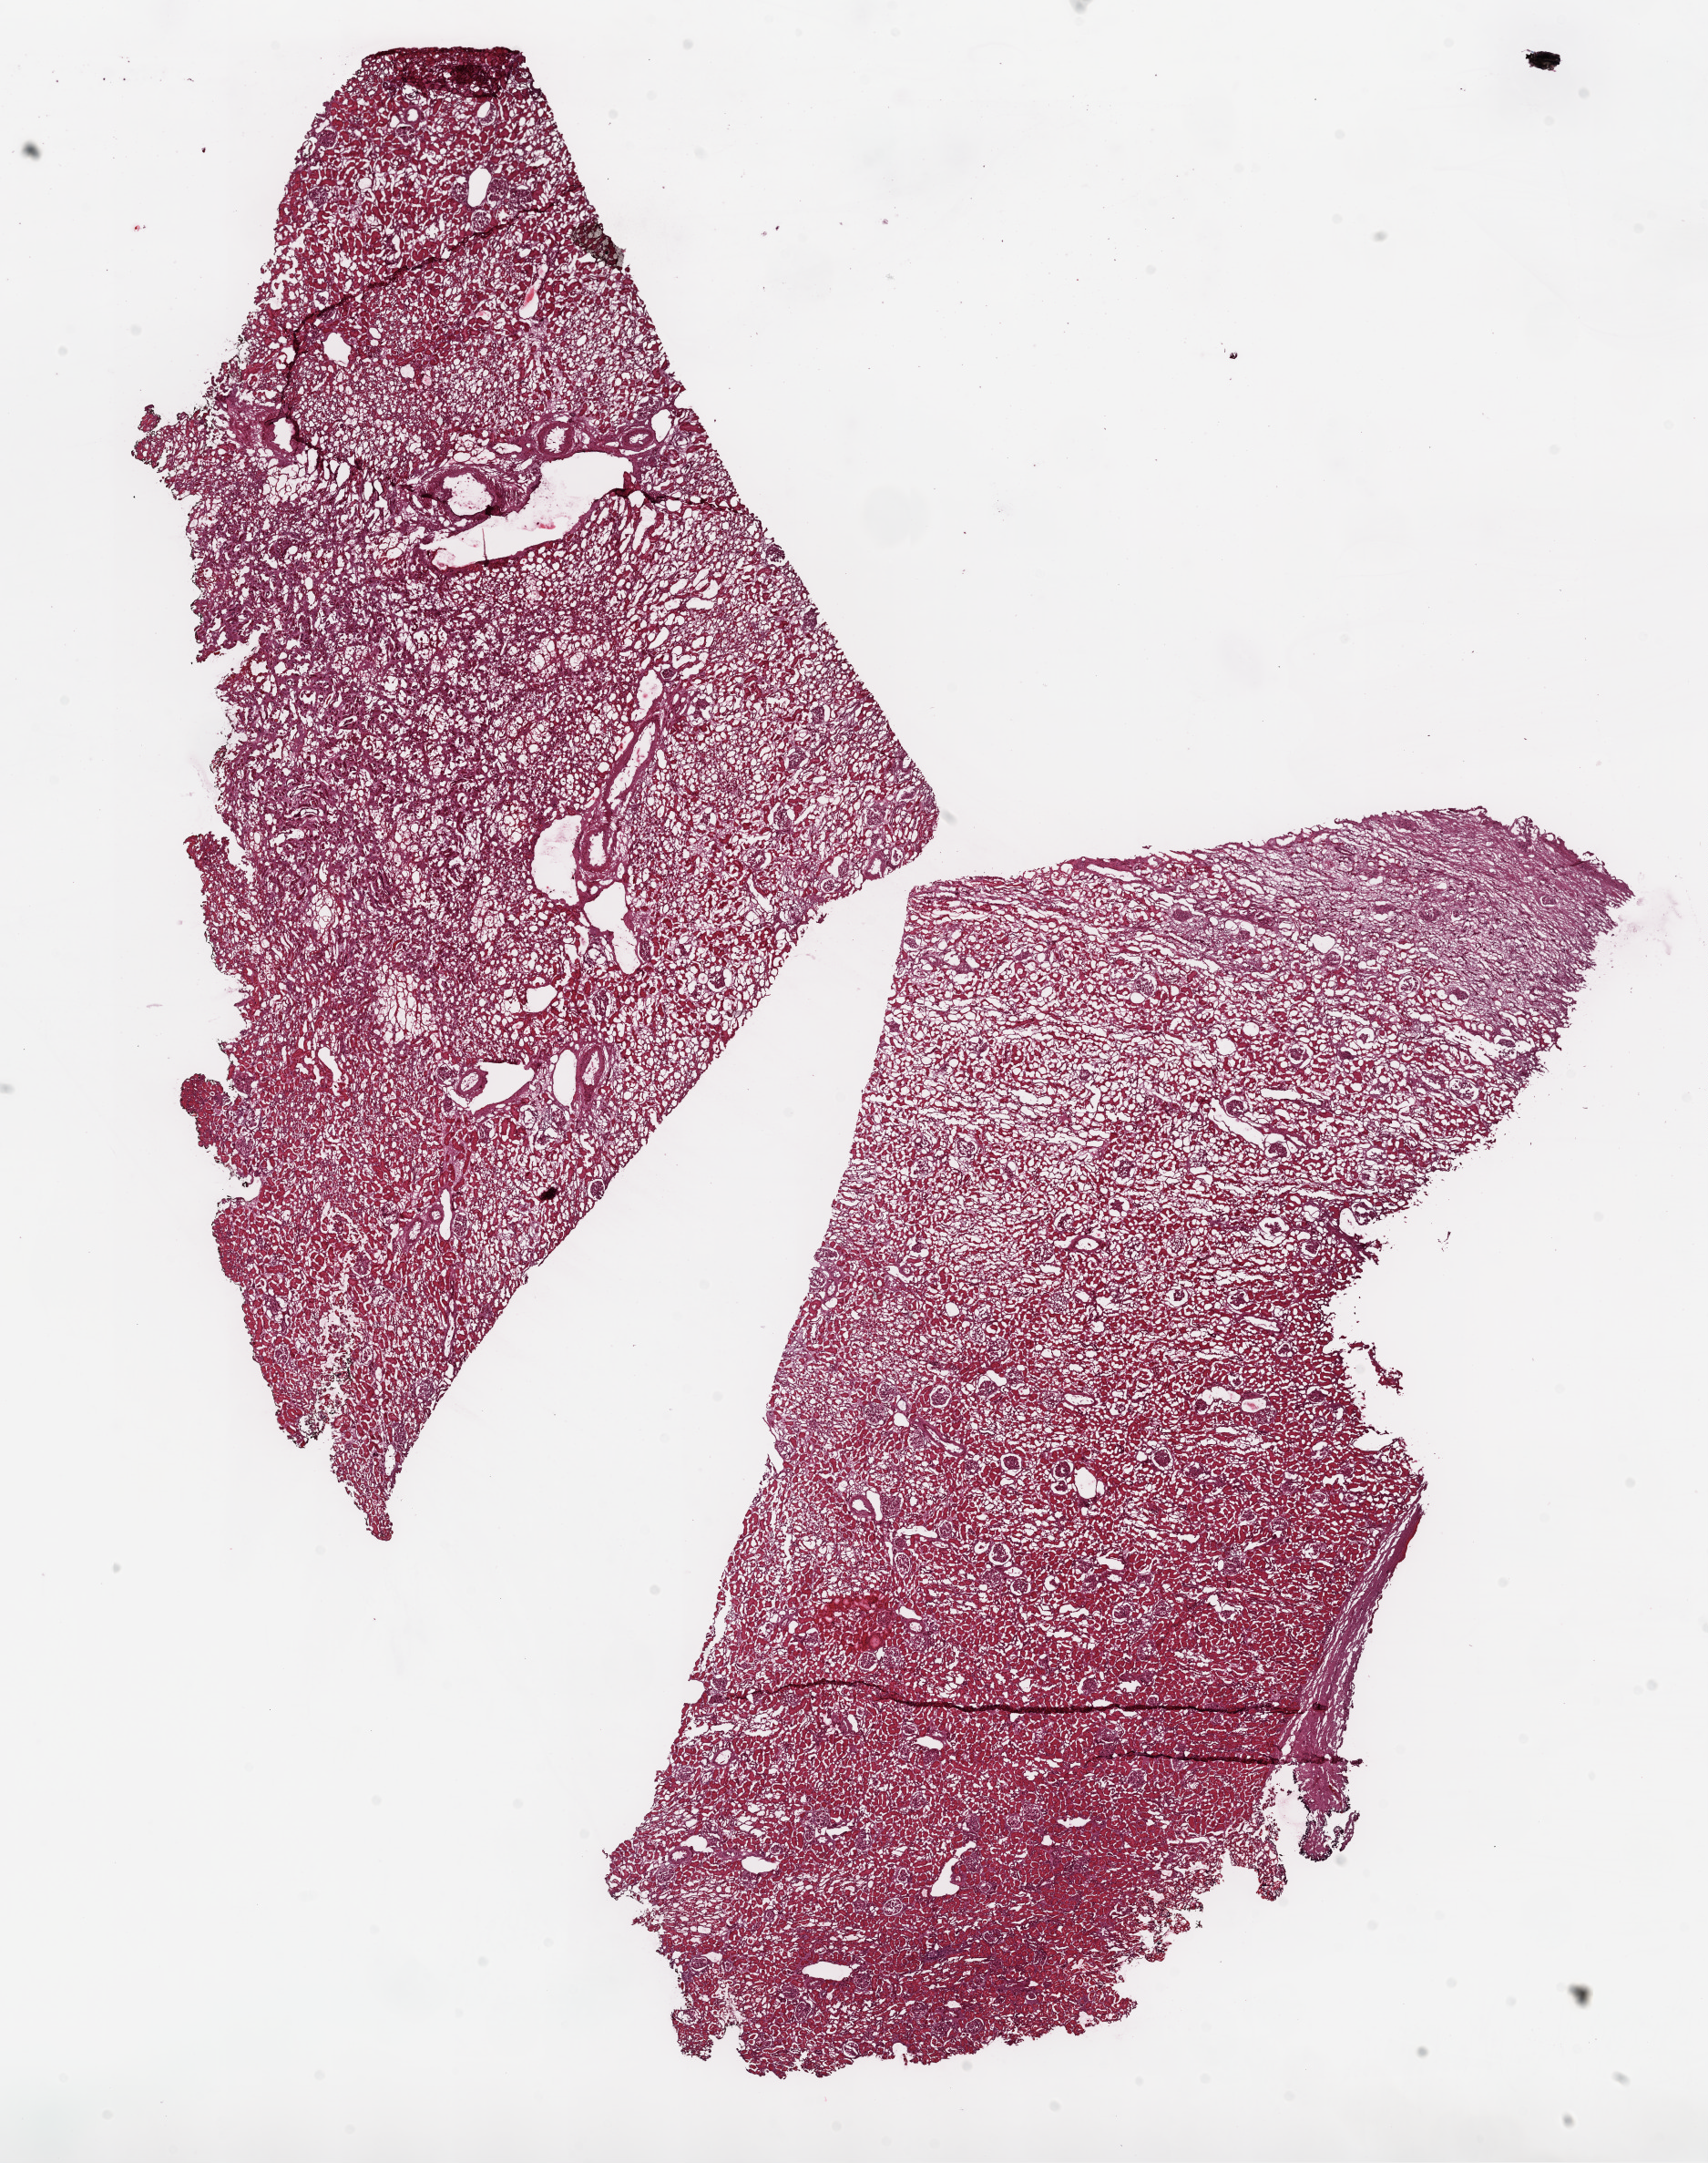
H&E whole-slide image — a low-resolution overview of the entire scanned area, about 15.0 x 19.0 mm, frozen section from the top of the tissue portion, solid tissue normal (non-tumour tissue) sample from the kidney. Patient: male, age at initial diagnosis 43 years.
* this section: solid tissue normal (non-tumour) sample from the same patient
* patient diagnosis: Clear cell adenocarcinoma, NOS